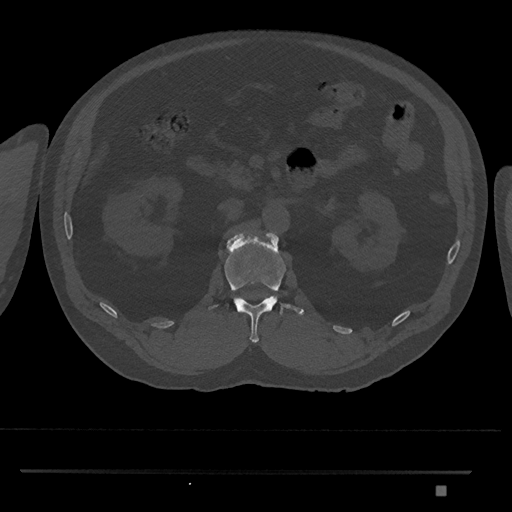
CT including the spine, one axial slice; position 813 of 1134 along the scan axis; reconstruction kernel Br40s/3; 120 kVp; bone window (W 1800 / L 400 HU); 0.5 mm slice thickness; 512 × 512 image matrix, field of view 429 × 429 mm. Patient: male, 65 years. From the clinical record (not read from this slice): primary cancer: prostate.
Structures marked on this image (semi-automatically segmented with operator editing):
- L1 vertebra: bounding box <209,231,304,343> (left, top, right, bottom; pixels)